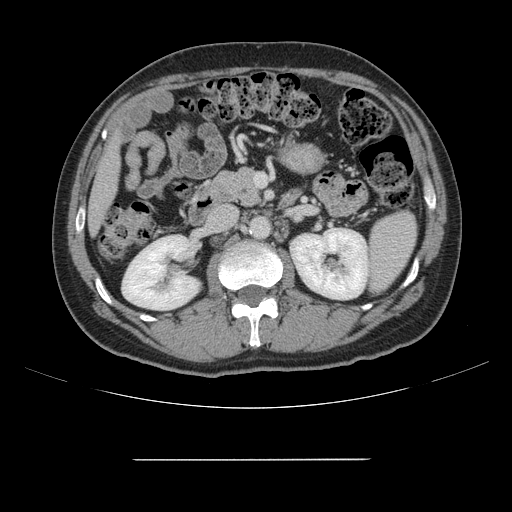
Contrast-enhanced abdominal CT, one axial slice. Slice 60 of 164 in the series (ordered by position). Soft-tissue window (W 400 / L 40 HU). 2.5 mm slice thickness. 512 × 512 image matrix. Male patient, age 54 years. From the clinical record (not read from this slice): diagnosis: colorectal cancer liver metastases, imaged before liver resection; multiple liver metastases: yes; largest metastasis: 1 cm; chemotherapy before resection: yes.
Annotated regions visible in this slice (outlined manually by an expert reader):
- liver: bounding box <89,141,119,231> (left, top, right, bottom; pixels)
- planned liver remnant (the part of the liver to remain after resection): <89,141,119,230>